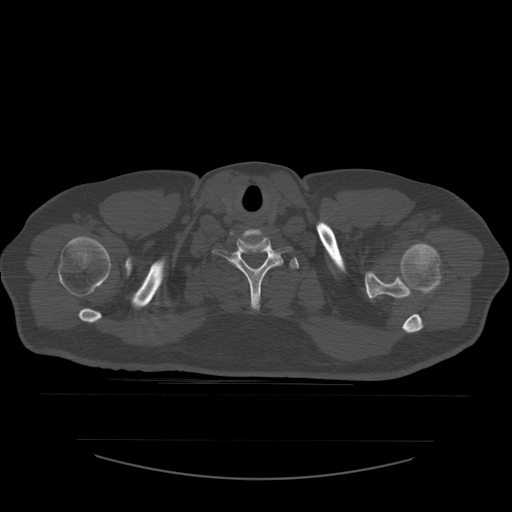
CT including the spine, one axial slice; position 481 of 532 along the scan axis; reconstruction kernel STANDARD; 120 kVp; bone window (W 1800 / L 400 HU); 1.25 mm slice thickness; 512 × 512 image matrix. Patient age 44 years. Case-level facts recorded for this patient, not image findings: primary cancer: soft tissue sarcoma.
Structures marked on this image (semi-automatically segmented with operator editing):
- T1 vertebra: bounding box <282,257,299,269> (left, top, right, bottom; pixels)